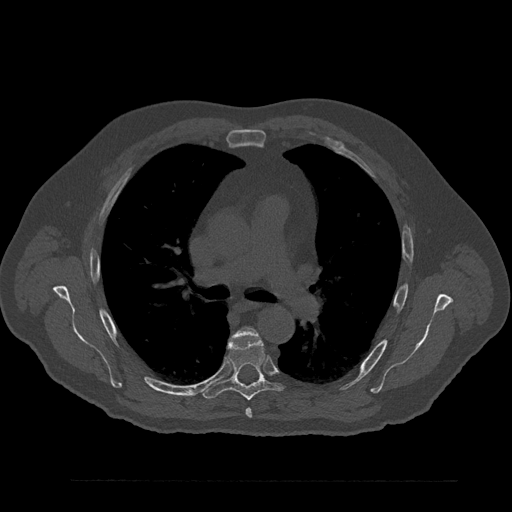
CT including the spine, one axial slice. Position 564 of 797 along the scan axis. Reconstruction kernel Br40s/3. 120 kVp. Bone window (W 1800 / L 400 HU). 0.5 mm slice thickness. 512 × 512 image matrix, field of view 430 × 430 mm. Male patient, age 61 years. Case-level facts recorded for this patient, not image findings: primary cancer: prostate.
Outlined on this slice (semi-automatically segmented with operator editing):
- T5 vertebra: box from (x=234, y=328) to (x=257, y=418) px
- T6 vertebra: (x=202, y=338)–(x=285, y=400)